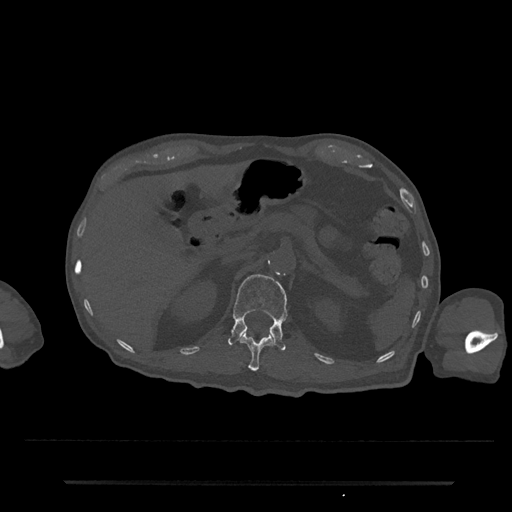
CT including the spine, one axial slice. Position 157 of 797 along the scan axis. 120 kVp. Bone window (W 1800 / L 400 HU). 0.5 mm slice thickness. 512 × 512 image matrix. Patient: male, 74 years. Case-level facts recorded for this patient, not image findings: primary cancer: prostate.
Annotated regions visible in this slice (semi-automatic segmentation, software-assisted and operator-edited):
- L1 vertebra: bounding box [x1, y1, x2, y2] px = [228, 274, 288, 351]
- T12 vertebra: [240, 333, 273, 371]